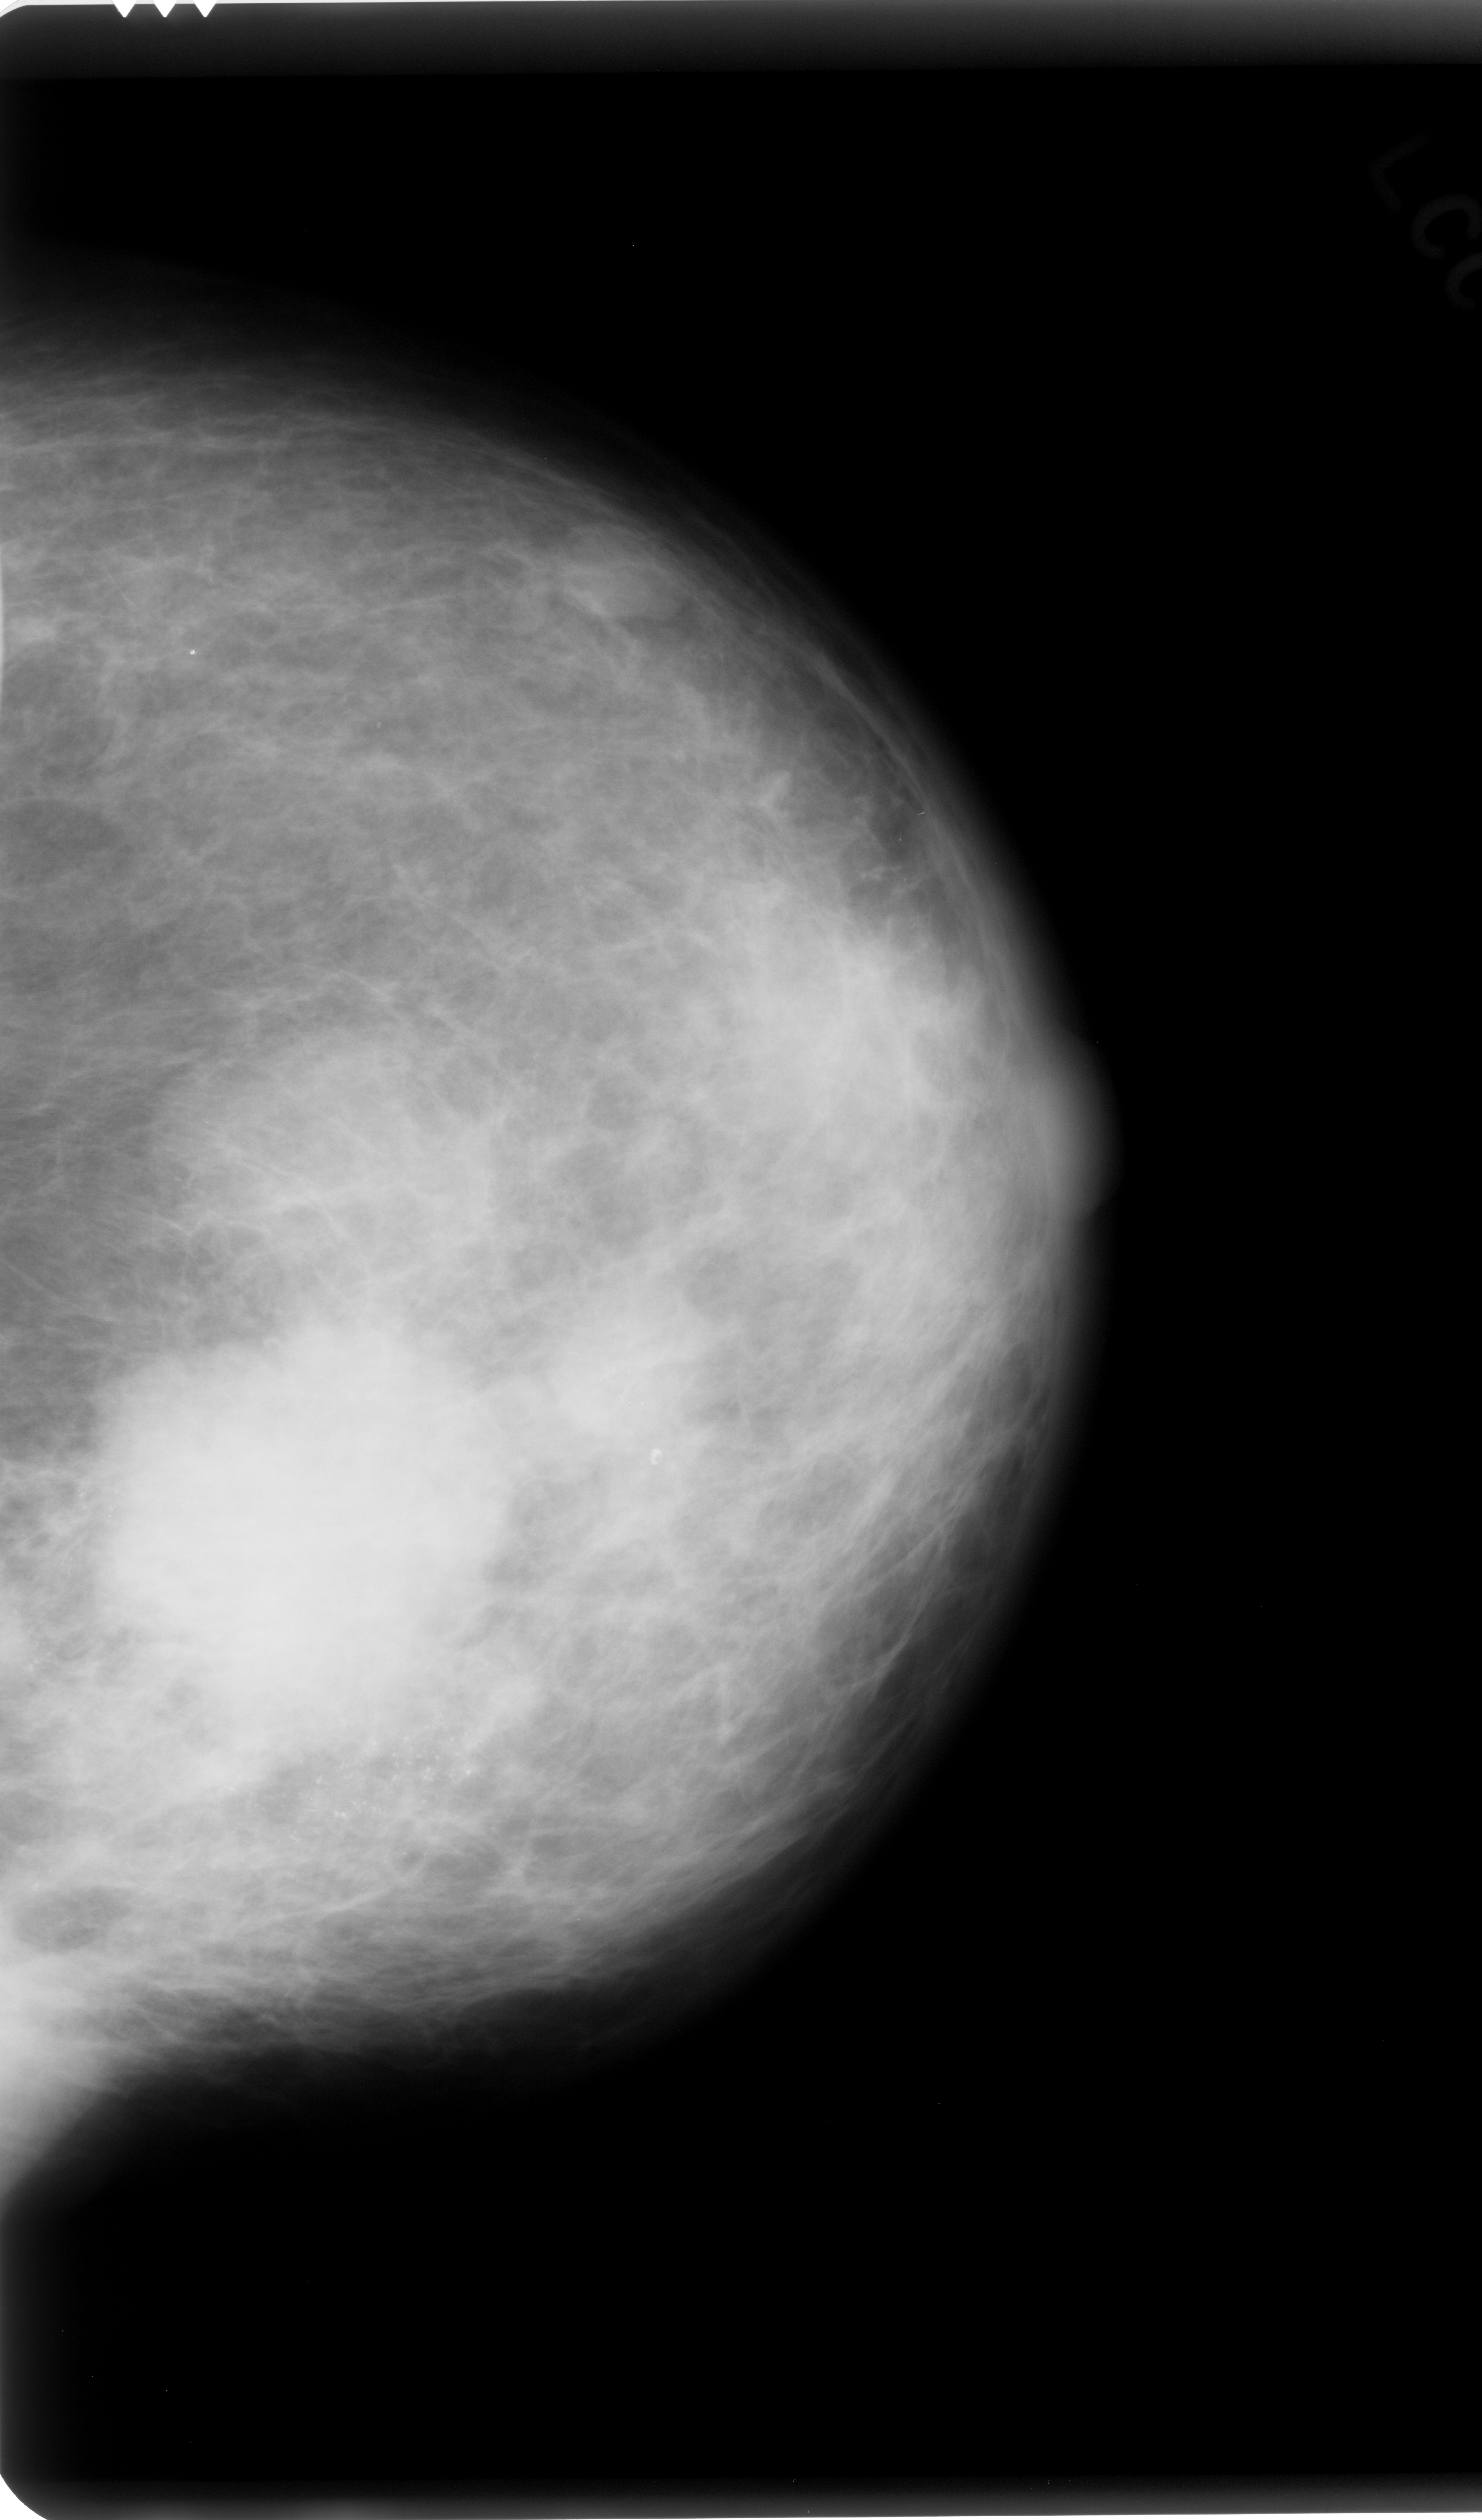
Scanned film-screen mammogram; left breast; CC view; breast composition: scattered fibroglandular densities (BI-RADS density category 2 of 4).
Abnormality record for this image: calcifications, morphology pleomorphic, distribution segmental; BI-RADS assessment category 5; subtlety rating 5 on a 1 (subtle) to 5 (obvious) scale; pathology result (as recorded, not read from the image): malignant.